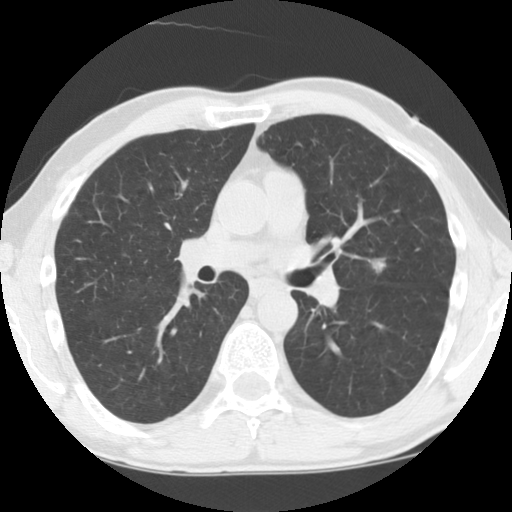
Axial slice from a low-dose chest CT screening exam. Baseline annual screen. Lung window (W 1500 / L -600 HU). 120 kVp. Slice 120 of 262 in the series. Male, age 55 years at enrolment. Current smoker at enrolment.
Expert-annotated lung lesion, bounding box <349,243,403,283> (left, top, right, bottom; pixels). The screening reader recorded 5 non-calcified nodules or masses ≥4 mm on this exam; which of them this box marks is not recorded. Lung cancer was diagnosed 59 days after this screen: large cell neuroendocrine carcinoma, left upper lobe, stage IA (AJCC 6th edition), 15 mm at pathology.